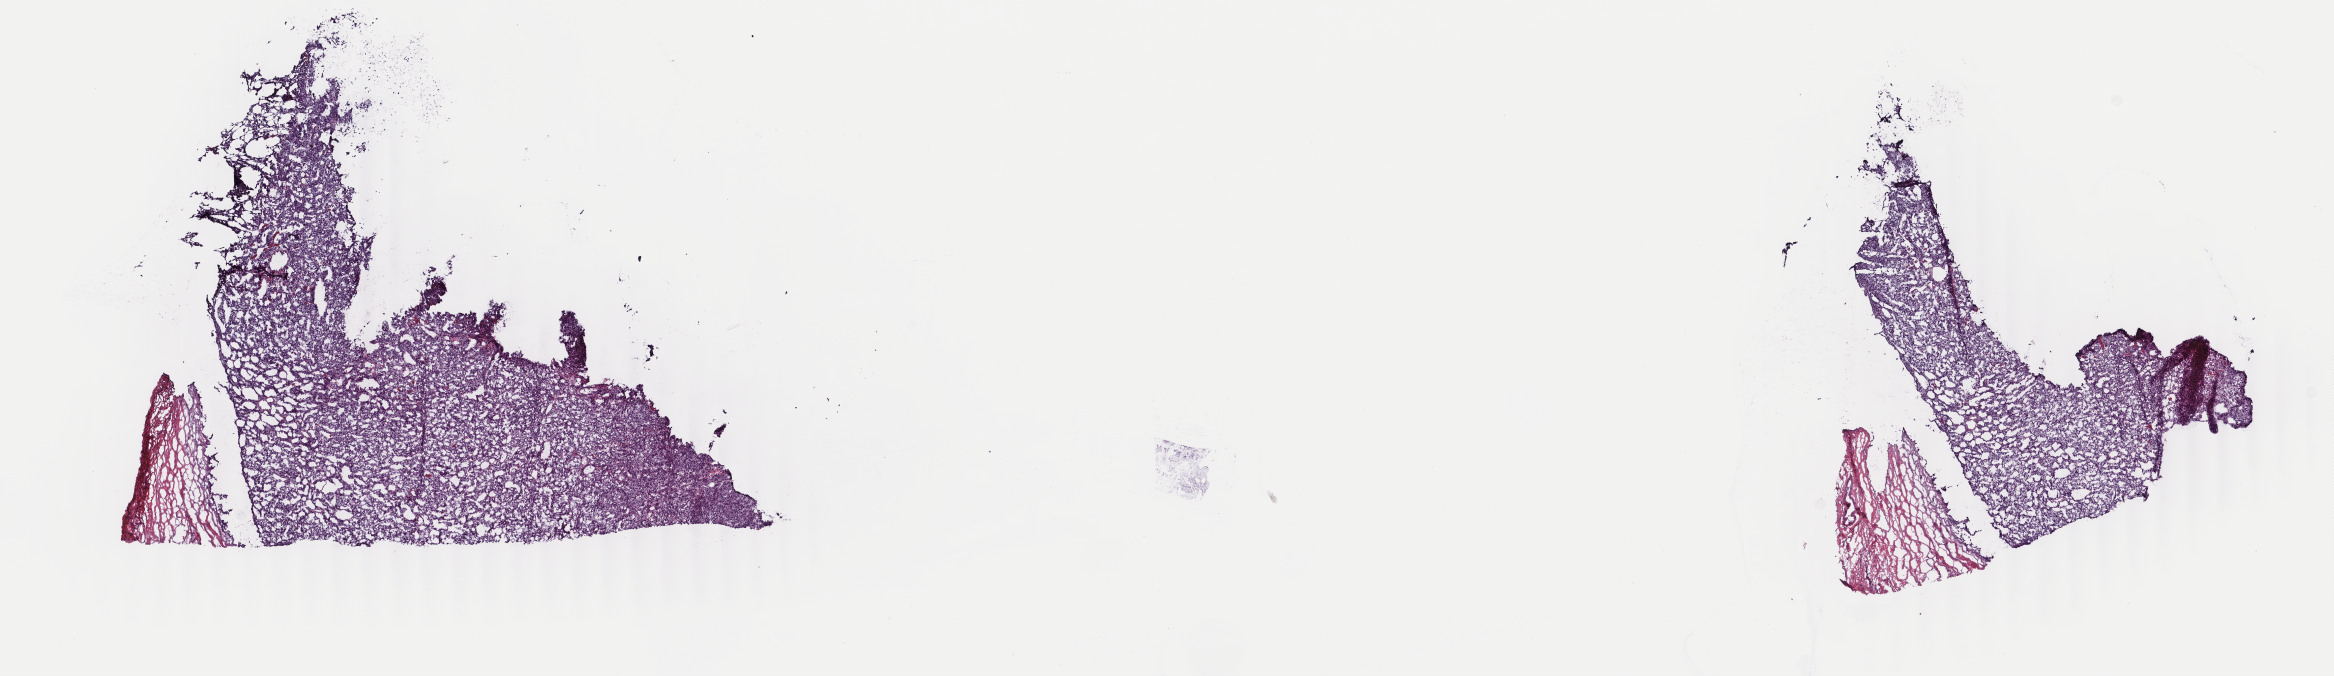
Whole-slide histology image, Hematoxylin and eosin (H&E) stained — shown as a low-resolution overview of the whole scanned area (about 18.6 x 5.4 mm), frozen section from the top of the tissue portion, primary tumour sample from the adrenal cortex. Patient: female, age at initial diagnosis 74 years.
Diagnosis: Adrenal cortical carcinoma (cortex of adrenal gland).